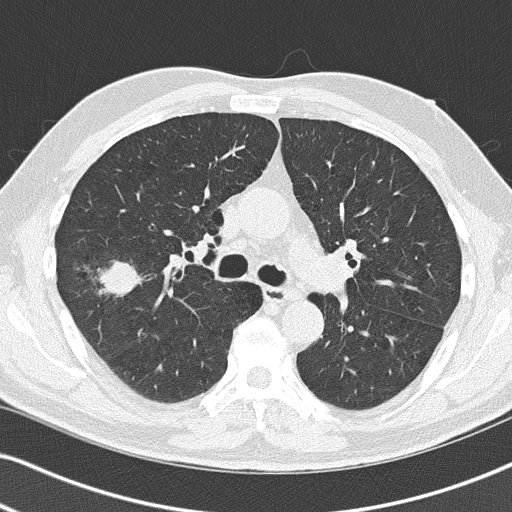
Low-dose screening chest CT, axial slice, first (baseline) screen, lung window (W 1500 / L -600 HU), 2 mm slice thickness, lung (sharp) reconstruction kernel (B50f), slice 59 of 140 in the series, 512 × 512 image matrix, field of view 330 × 330 mm. Male, age 67 years at enrolment. Former smoker at enrolment.
Lesion marked by an expert reader, bounding box <71,253,147,318> (left, top, right, bottom; pixels). The exam's reader record, not a measurement of the box and not confirmed to be the same lesion: non-calcified nodule or mass ≥4 mm, right upper lobe, 26 × 24 mm, spiculated (stellate) margins, soft tissue attenuation. Later outcome: lung cancer diagnosed 49 days after this screen — squamous cell carcinoma, NOS, right upper lobe, poorly differentiated (G3), stage IA (AJCC 6th edition), 27 mm at pathology.